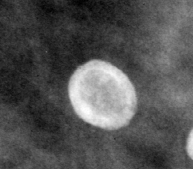
Region of interest cut from a scanned film mammogram (one marked finding), left breast, MLO view, BI-RADS breast density category 3 (scale 1–4).
- Marked abnormality: calcifications, morphology round and regular / eggshell; BI-RADS assessment category 2; subtlety rating 3 on a 1 (subtle) to 5 (obvious) scale; benign; no additional work-up was recommended (benign without callback).